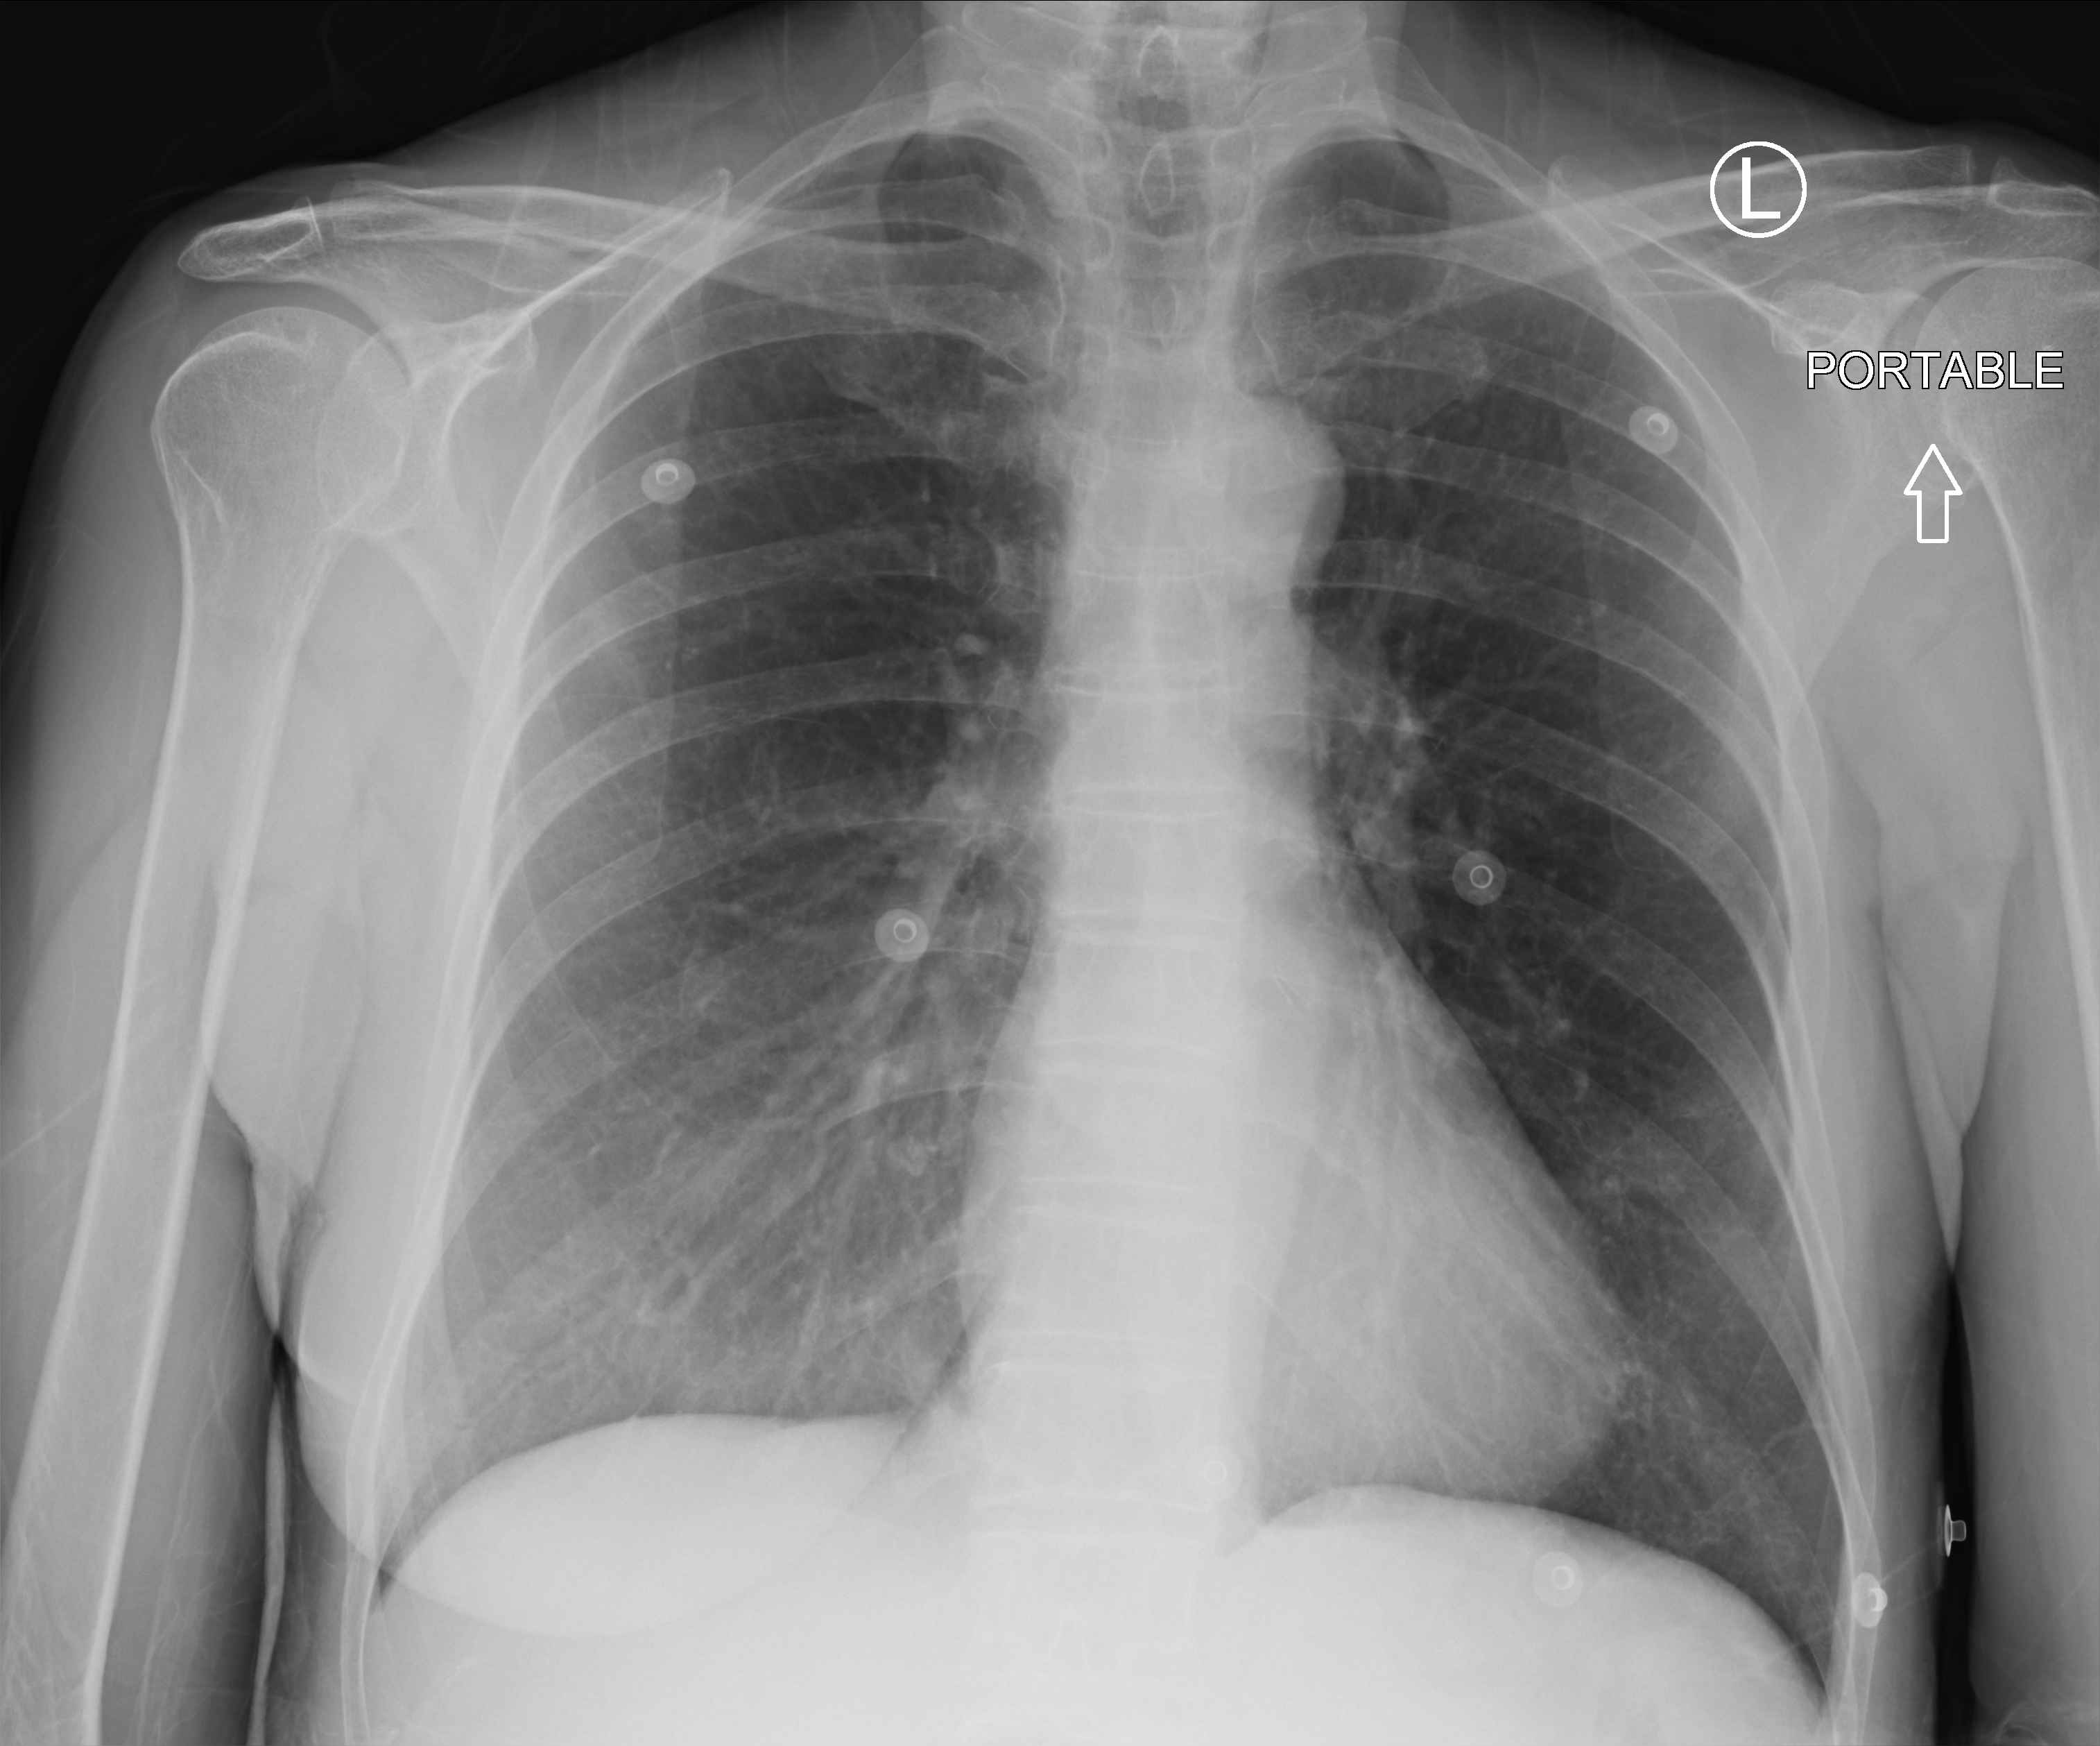
Bedside chest radiograph (computed radiography); anteroposterior (AP) projection. Patient hospitalised with COVID-19; female, aged 60–74 years.
Hospital-stay facts (about this admission, not read from this image; timing relative to this image not recorded):
- COPD (admission record): no
- admitted to intensive care during this hospital stay: no
- mechanically ventilated during this hospital stay: no